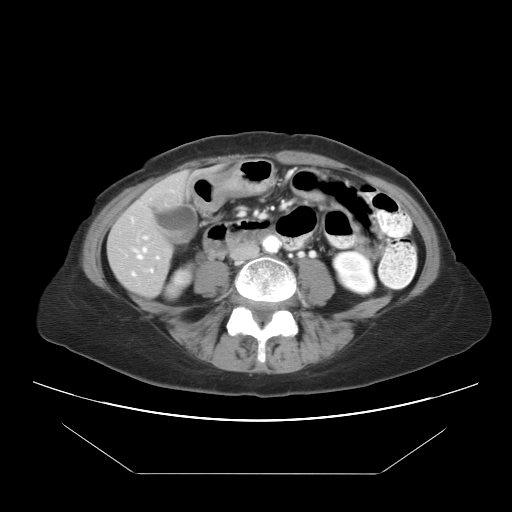
Contrast-enhanced abdominal CT, one axial slice; position 3 of 21 along the scan axis; reconstruction kernel STANDARD; intravenous contrast given; soft-tissue window (W 400 / L 40 HU); 7.5 mm slice thickness; 512 × 512 image matrix, field of view 392 × 392 mm. Female patient, age 72 years. Case-level facts recorded for this patient, not image findings: diagnosis: colorectal cancer liver metastases, imaged before liver resection; multiple liver metastases: yes; largest metastasis: 4 cm; chemotherapy before resection: yes.
Outlined on this slice (outlined manually by an expert reader):
- hepatic veins: bounding box (x1, y1, x2, y2) in pixels: (132, 248, 146, 275)
- liver: (108, 176, 183, 296)
- planned liver remnant (the part of the liver to remain after resection): (108, 176, 183, 294)